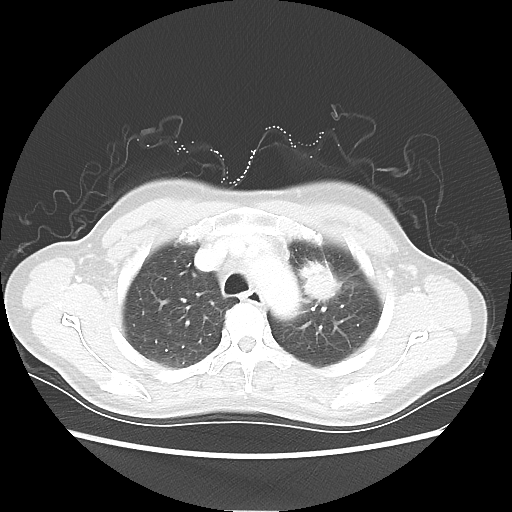
Chest CT, one axial slice; slice 42 of 54 in the series (ordered by position); 80 kVp; lung window (W 1500 / L -600 HU); 5 mm slice thickness; 512 × 512 image matrix, field of view 360 × 360 mm. Patient: female, 53 years. Case-level facts recorded for this patient, not image findings: clinical TNM (as recorded): T1c N0 M0.
Outlined on this slice (bounding box drawn by a radiologist):
- lung tumour (recorded histology: adenocarcinoma): bounding box (x1, y1, x2, y2) in pixels: (292, 255, 342, 310)
- lung tumour (recorded histology: adenocarcinoma): (300, 252, 344, 306)